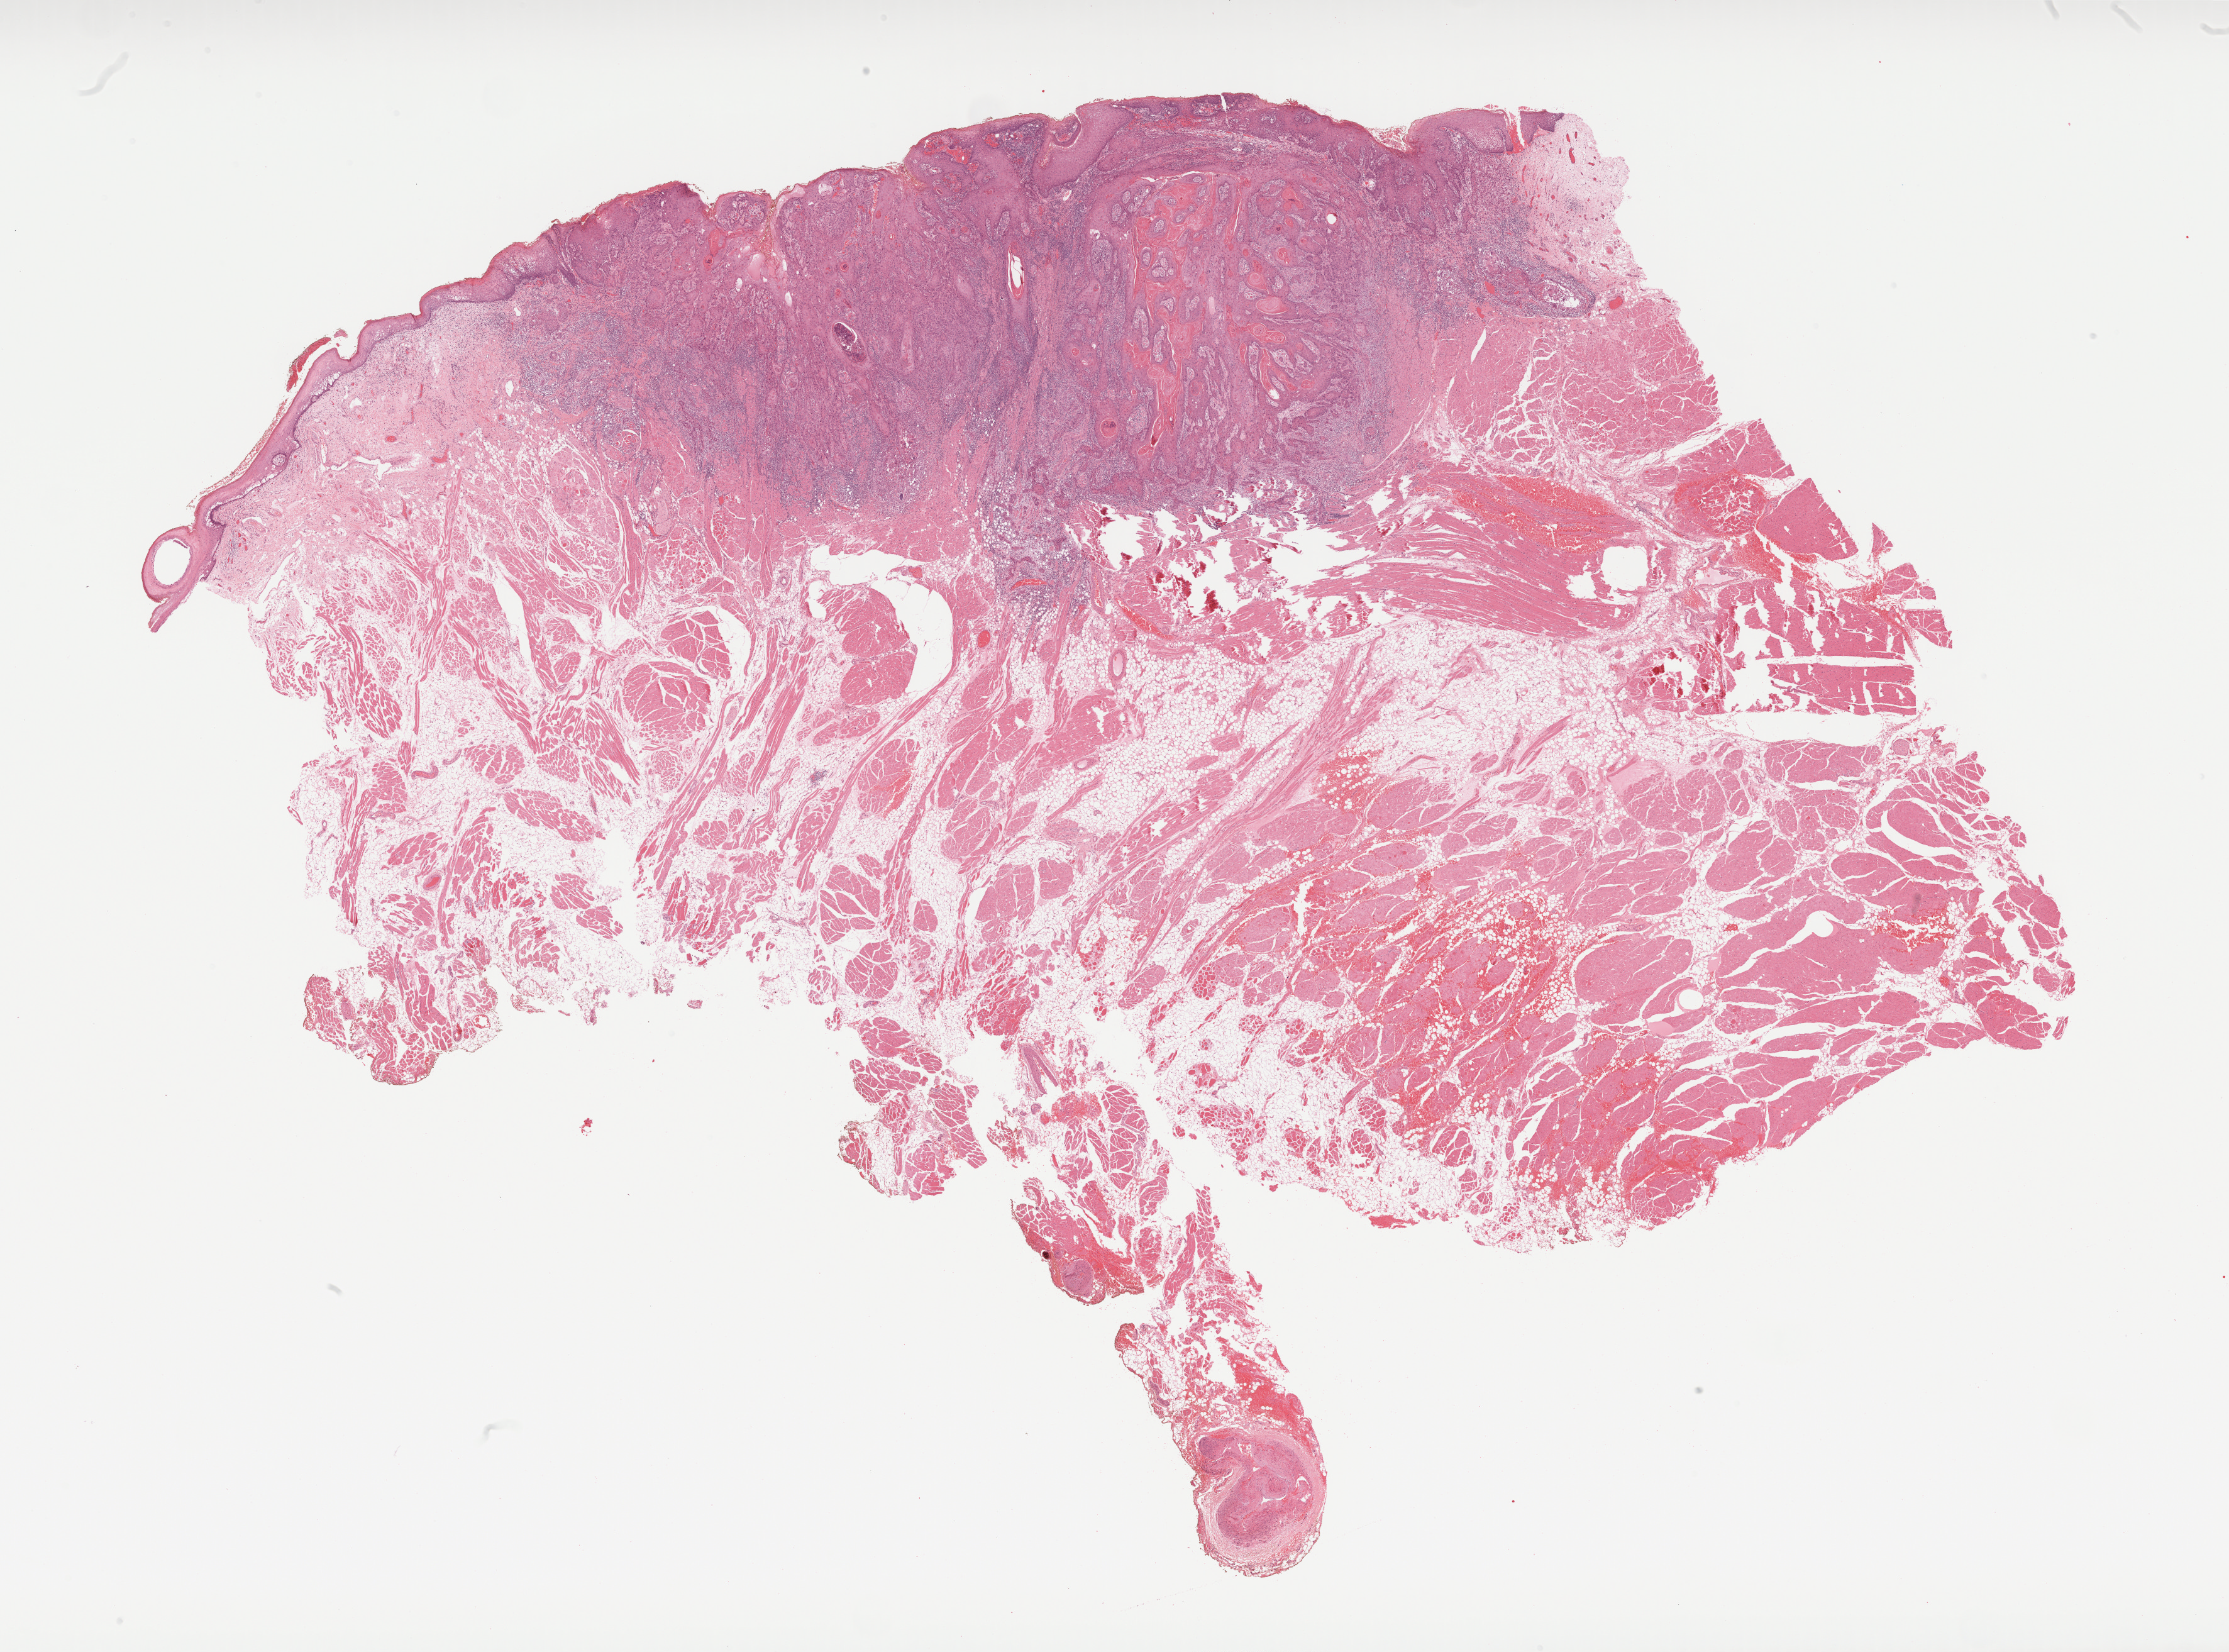
H&E-stained whole-slide image, shown as a low-resolution overview of the whole scanned area (about 28.6 x 21.2 mm), formalin-fixed paraffin-embedded (FFPE) diagnostic section, primary tumour sample from the head and neck. Patient: male, age at initial diagnosis 61 years. Histologic grade: G2 (moderately differentiated).
AJCC pathologic stage: II (6th edition). Histologic diagnosis: Squamous cell carcinoma, NOS (tongue, NOS). TNM: T2 N0.